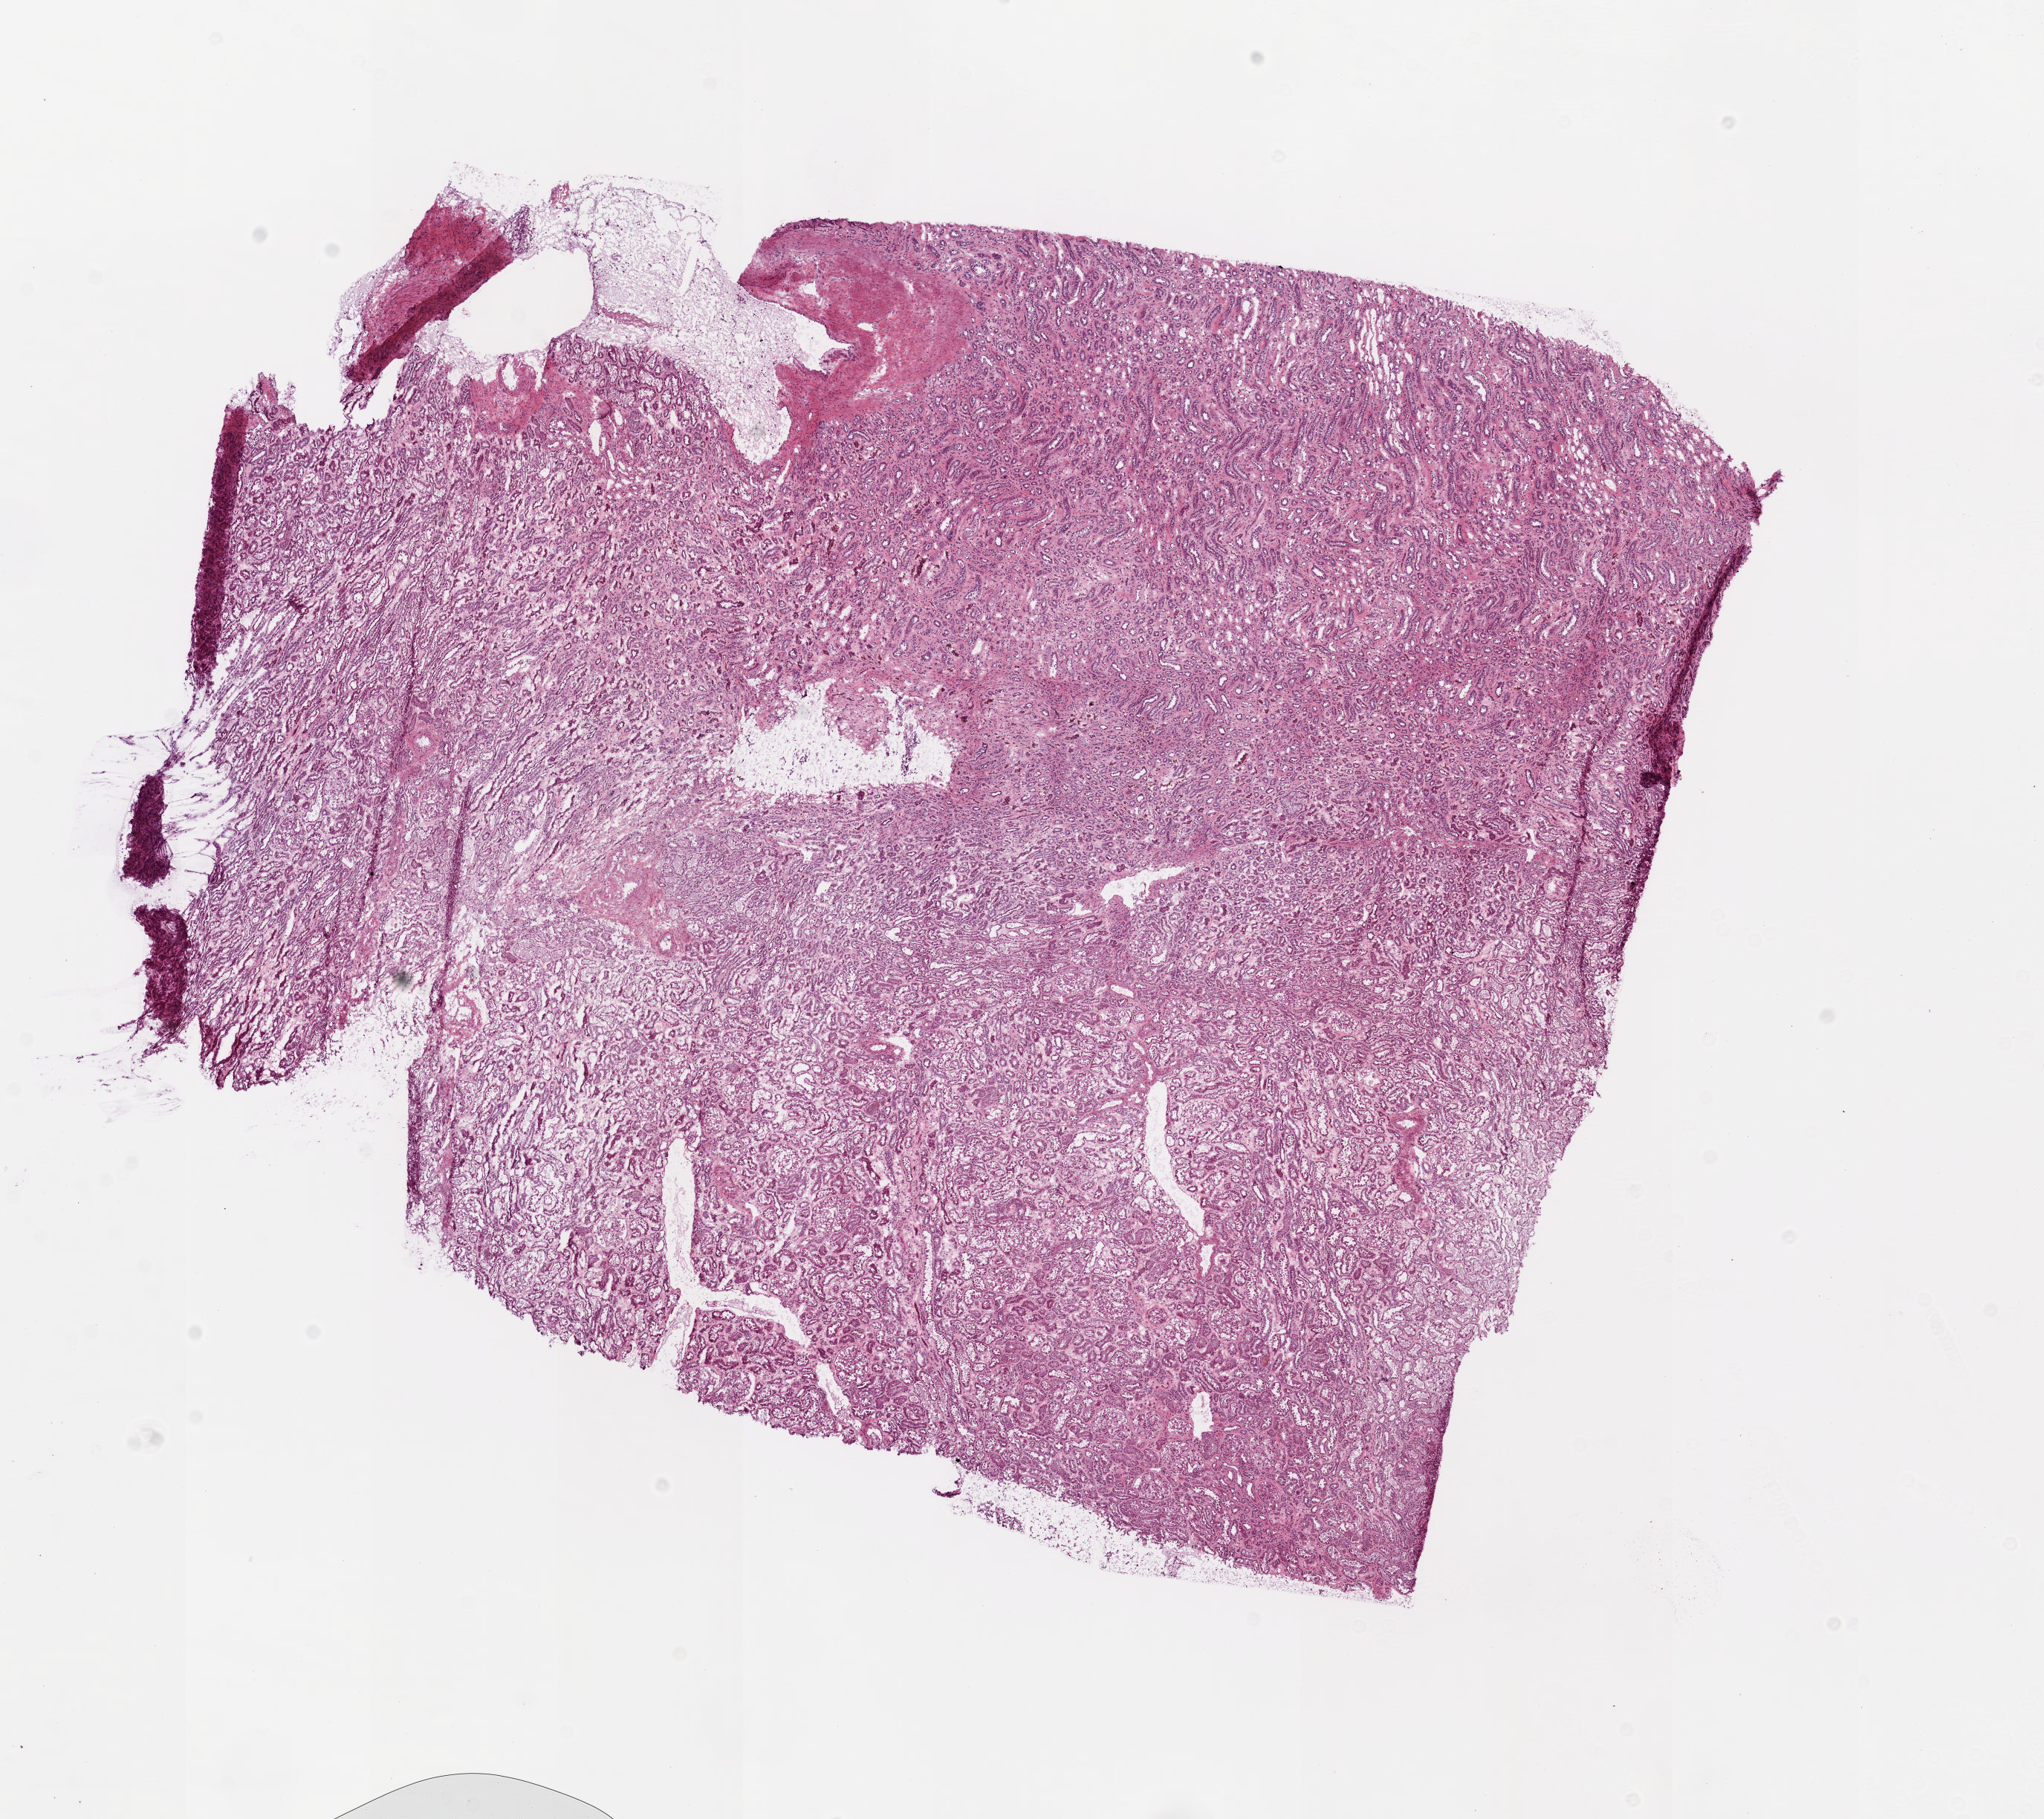
Digitized H&E tissue section (whole slide), low-resolution overview of the scanned area, about 10.9 x 9.7 mm (from a 20x scan). Frozen section from the top of the tissue portion. Solid tissue normal (non-tumour tissue) sample from the kidney. Male patient; age at initial diagnosis 46 years.
* this section: solid tissue normal sample (biorepository sample class)
* patient diagnosis: Clear cell adenocarcinoma, NOS